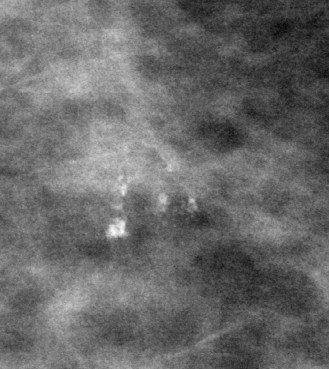
Region of interest cut from a scanned film mammogram (one marked finding); left breast; MLO view; BI-RADS breast density category 1 (scale 1–4).
Finding: calcifications, morphology pleomorphic, distribution clustered; BI-RADS assessment category 4; pathology (as recorded): benign.